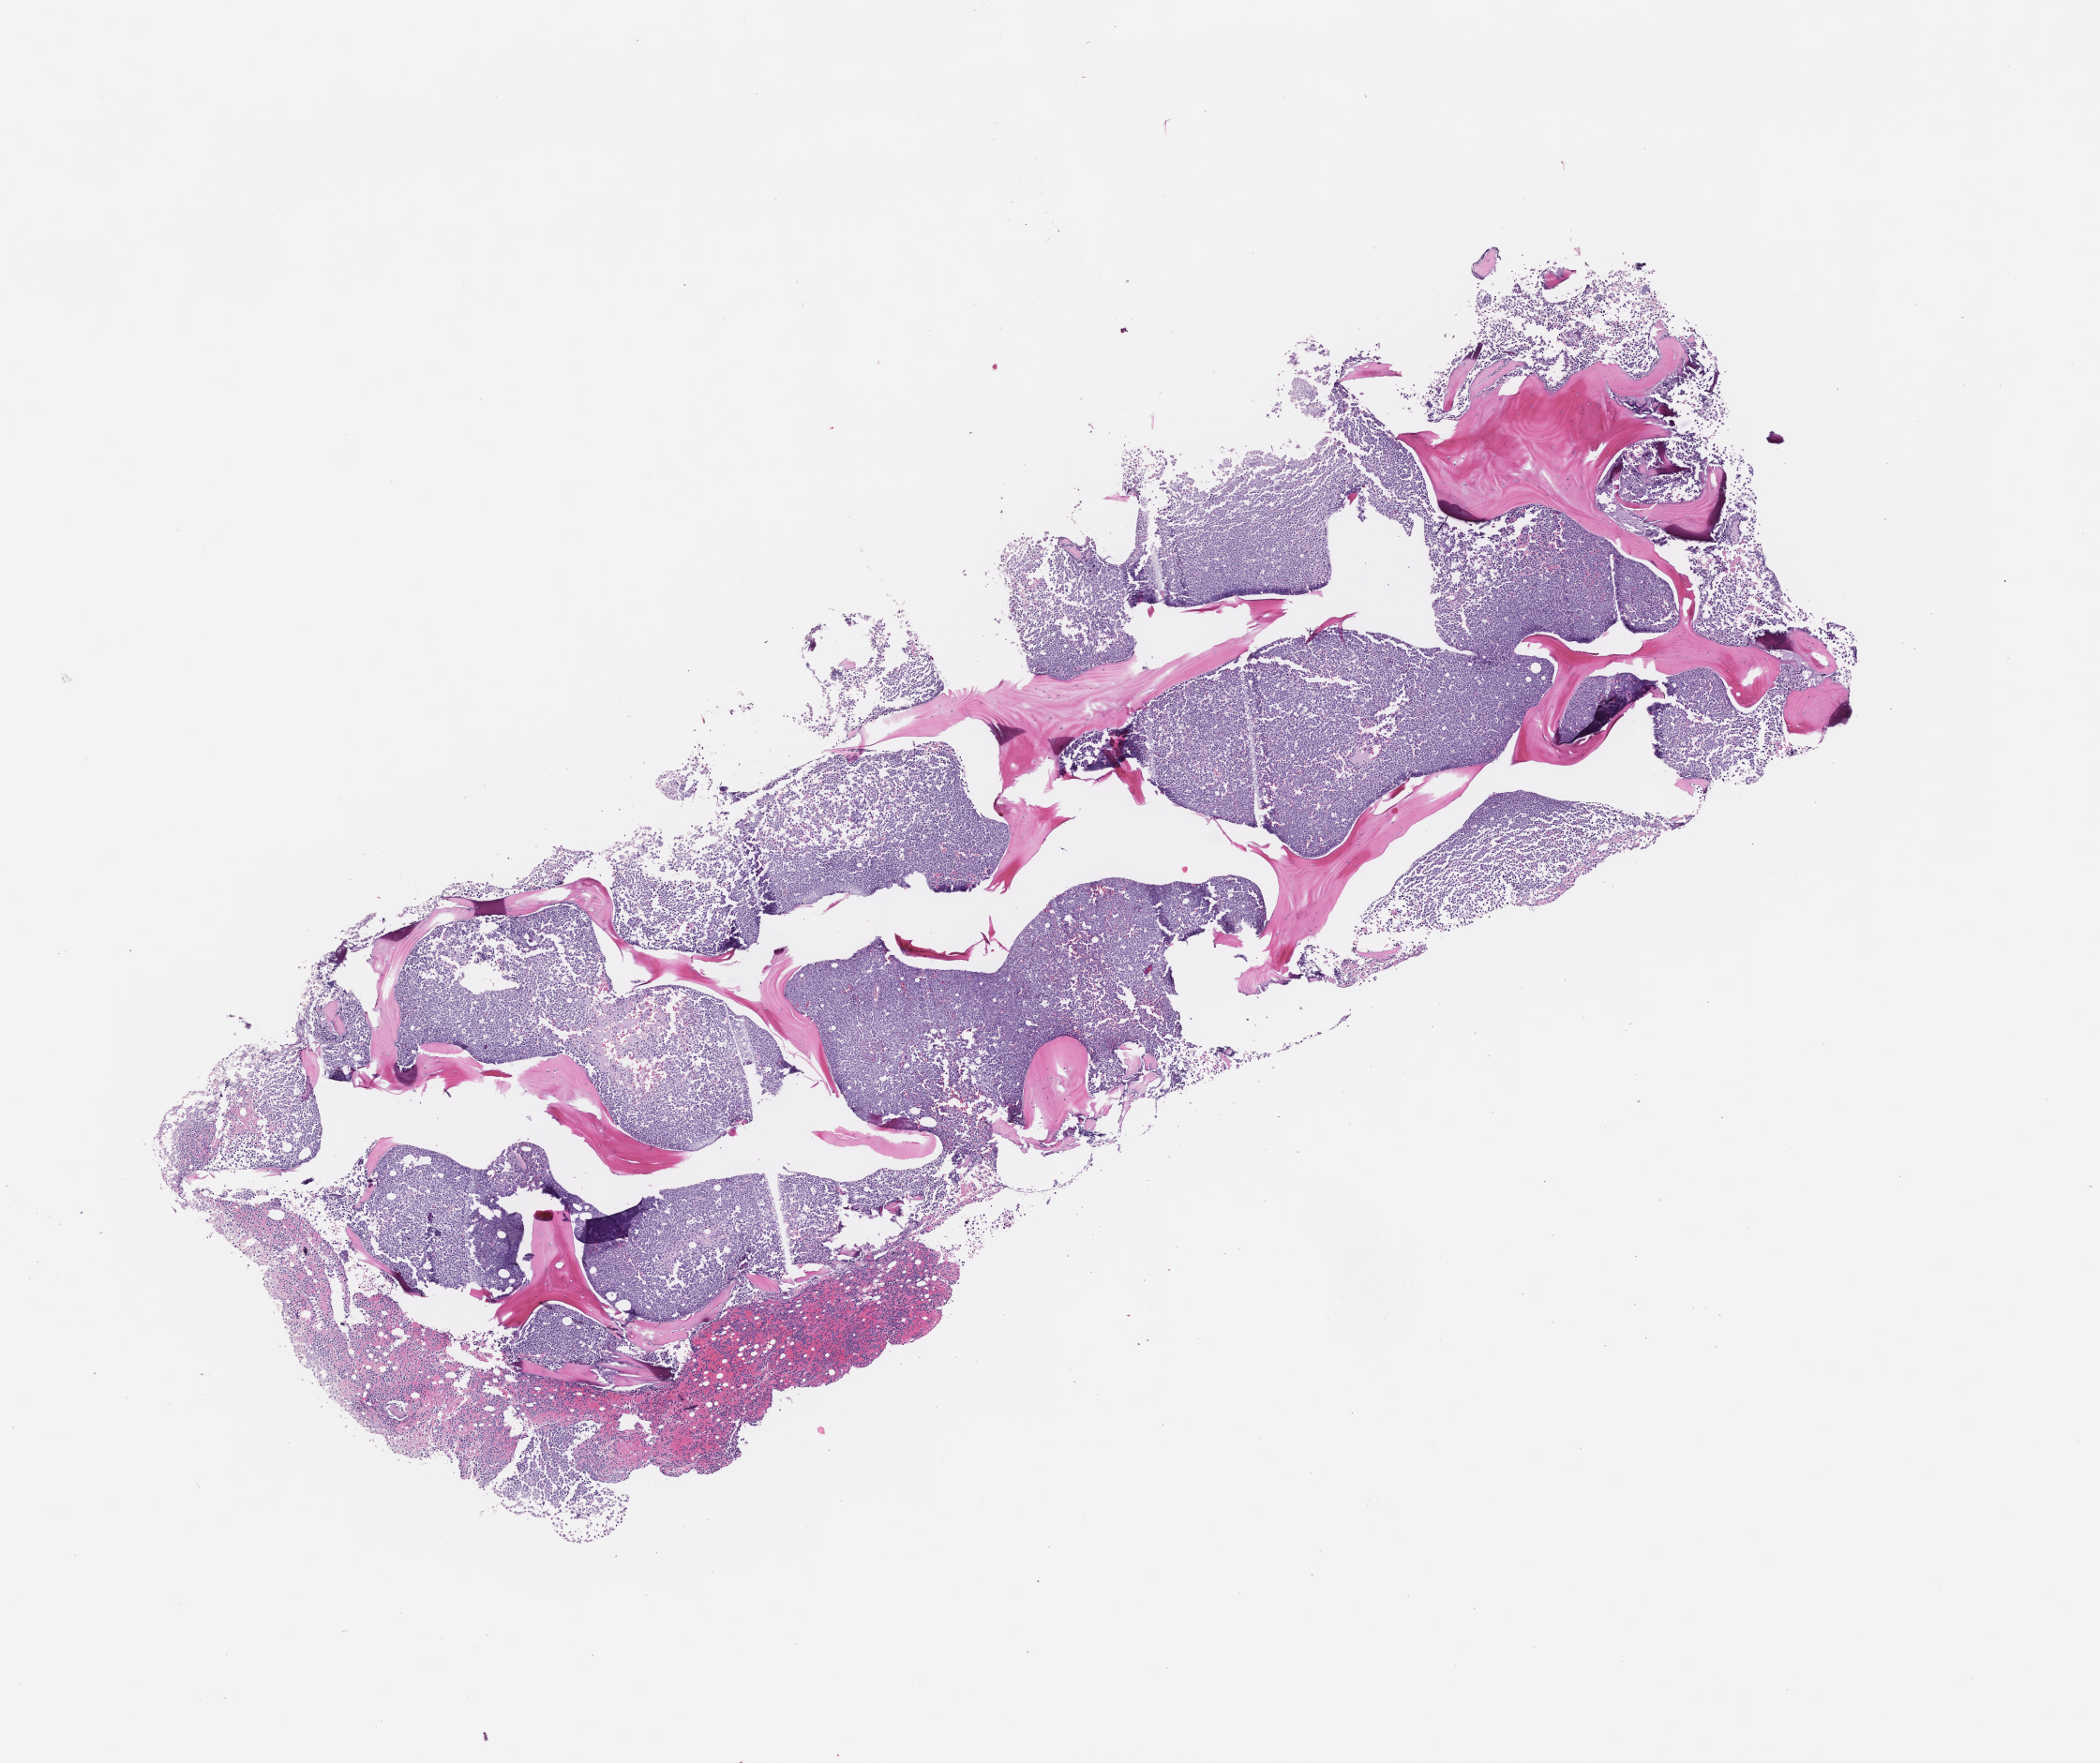
H&E whole-slide image, shown as a low-resolution overview of the whole scanned area (about 9.0 x 7.6 mm); FFPE section; tissue site: bone marrow; specimen time point: collected at baseline (before treatment). Patient: female.
This section: primary tumor. Diagnosis: Acute Myeloid Leukemia Not Otherwise Specified.